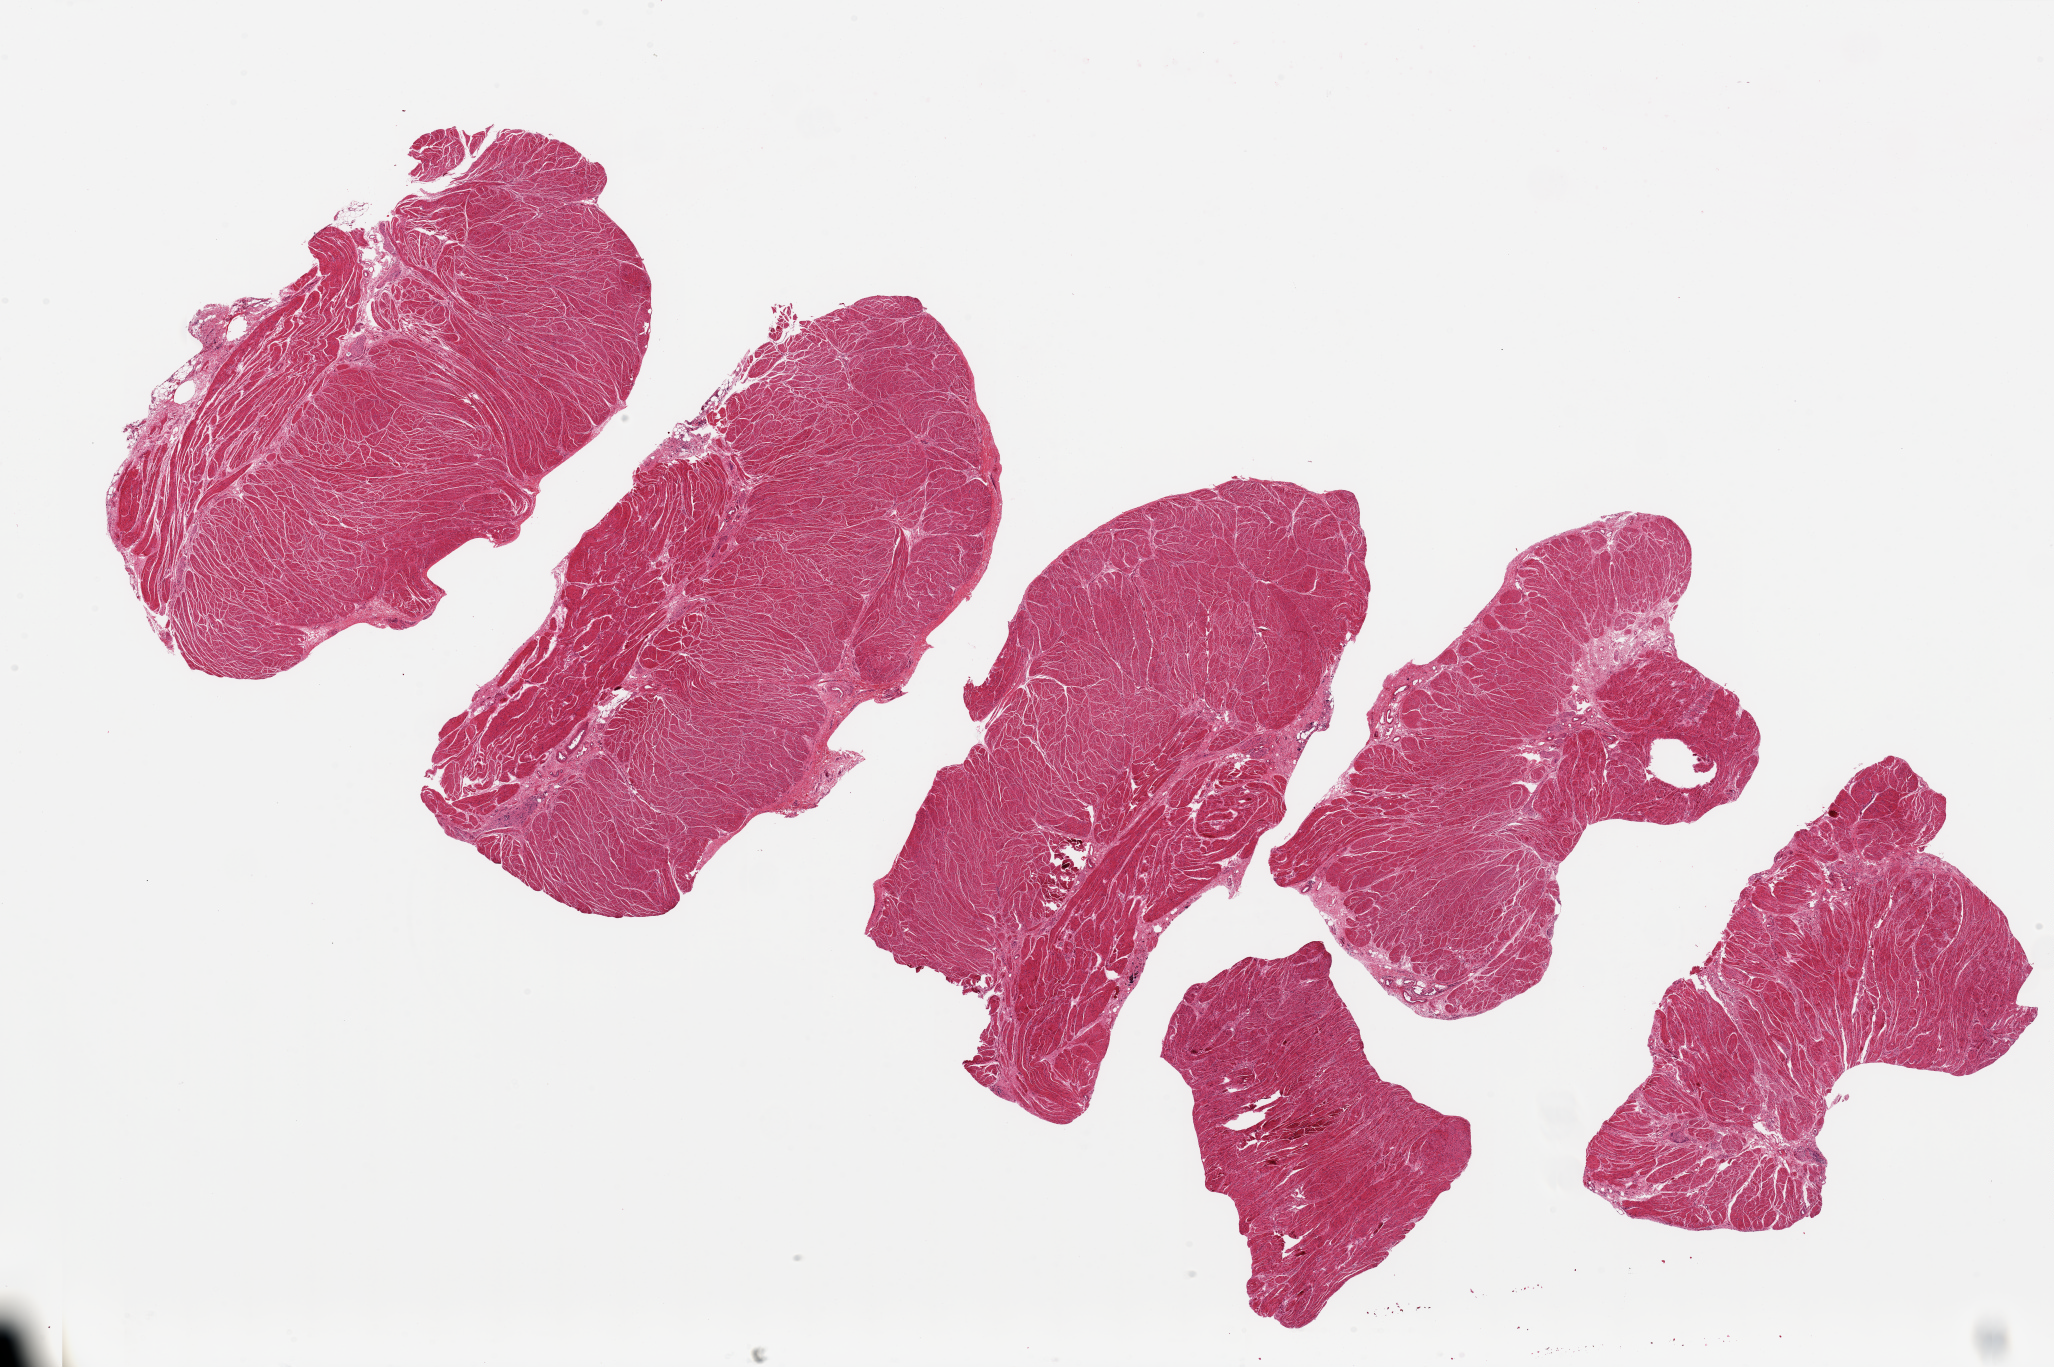
Digitized hematoxylin and eosin (H&E)-stained section, brightfield, a low-resolution overview of the entire scanned area, about 32.5 x 21.6 mm (from a 20x scan). PAXgene-fixed paraffin-embedded (PFPE) section. Section of esophageal muscle (target tissue). Tissue donor sample. Female donor.
- pathologist's review note for this sample: 6 pieces, ~5-10x4mm